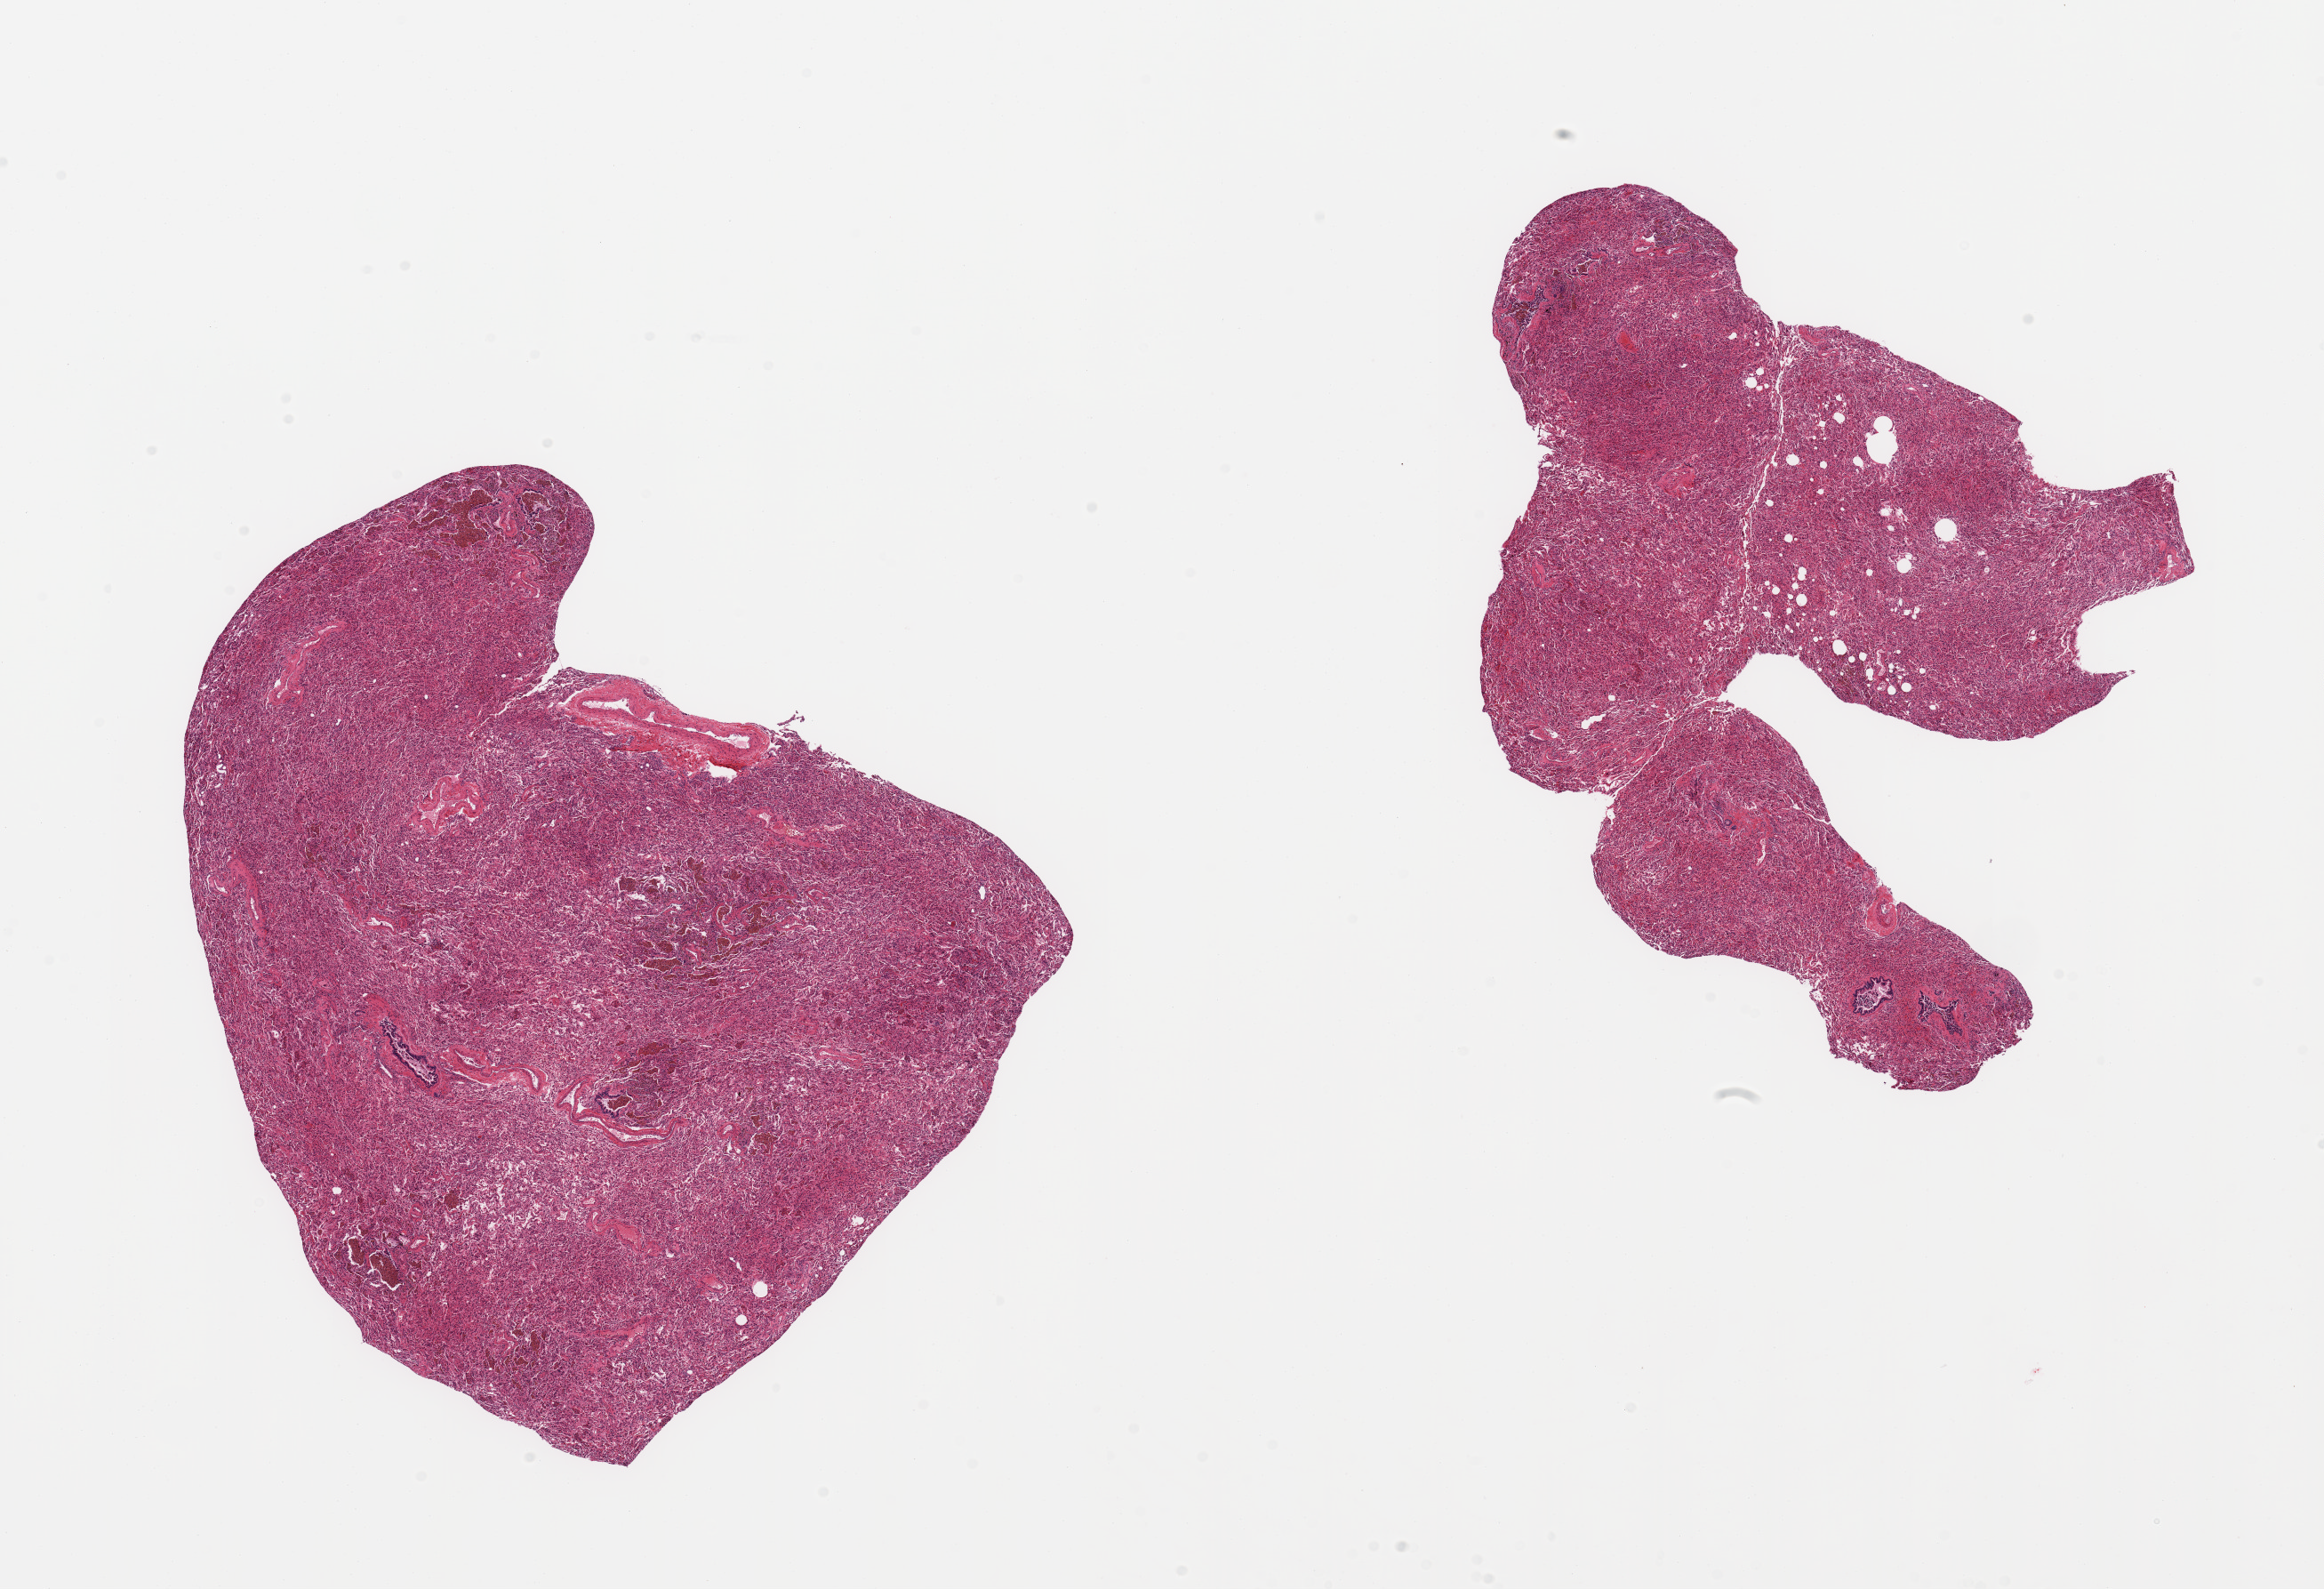
Hematoxylin and eosin (H&E) whole-slide image — low-resolution overview of the scanned area, about 20.7 x 14.1 mm. PAXgene-fixed paraffin-embedded (PFPE) section. Section of lung (target tissue). Tissue donor sample.
Pathologist's review note for this sample: 2 pieces; mild to focally moderate autolysis; bronchioles and alveoli filled with hemosiderinophages; collapsed alveolar spaces (atelectasis).